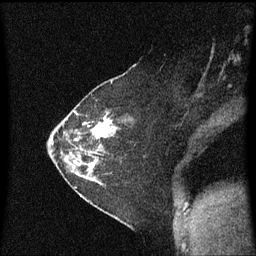
Breast MRI (dynamic contrast-enhanced), one sagittal slice. Position 37 of 60 along the scan axis. Dynamic contrast-enhanced series, image 2 of 3 at this slice position (ordered by acquisition). 1.5 T. TE 4.2 ms, TR 8.4 ms. 2 mm slice thickness. 256 × 256 image matrix, field of view 200 × 200 mm. Female patient, age 36 years. From the clinical record (not read from this slice): setting: breast cancer imaged before/during neoadjuvant chemotherapy; receptor status: HR-positive, HER2-negative.
Outlined on this slice (semi-automatically segmented with operator editing):
- analysis volume of interest (the breast-tissue region the enhancement analysis was run in; not a lesion): box from (x=66, y=102) to (x=117, y=179) px
- tumour enhancement mask (voxels above the 70 % enhancement threshold inside the analysis volume of interest): (x=89, y=118)–(x=116, y=173)